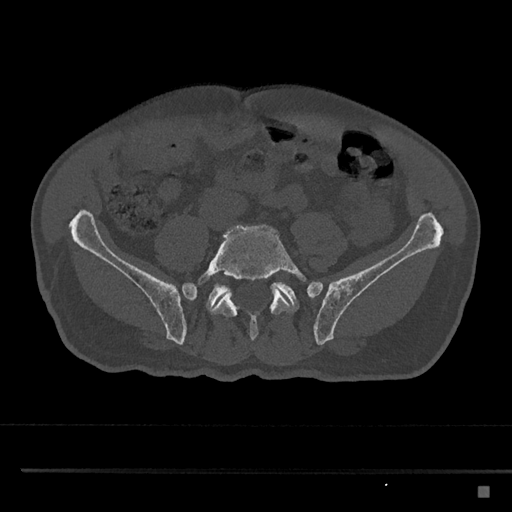
CT including the spine, one axial slice; slice 571 of 797 in the series (ordered by position); 120 kVp; bone window (W 1800 / L 400 HU); 0.5 mm slice thickness; 512 × 512 image matrix. Male patient, age 59 years. From the clinical record (not read from this slice): primary cancer: prostate.
Structures marked on this image (semi-automatic segmentation, software-assisted and operator-edited):
- L5 vertebra: bounding box (x1, y1, x2, y2) in pixels: (185, 225, 307, 341)